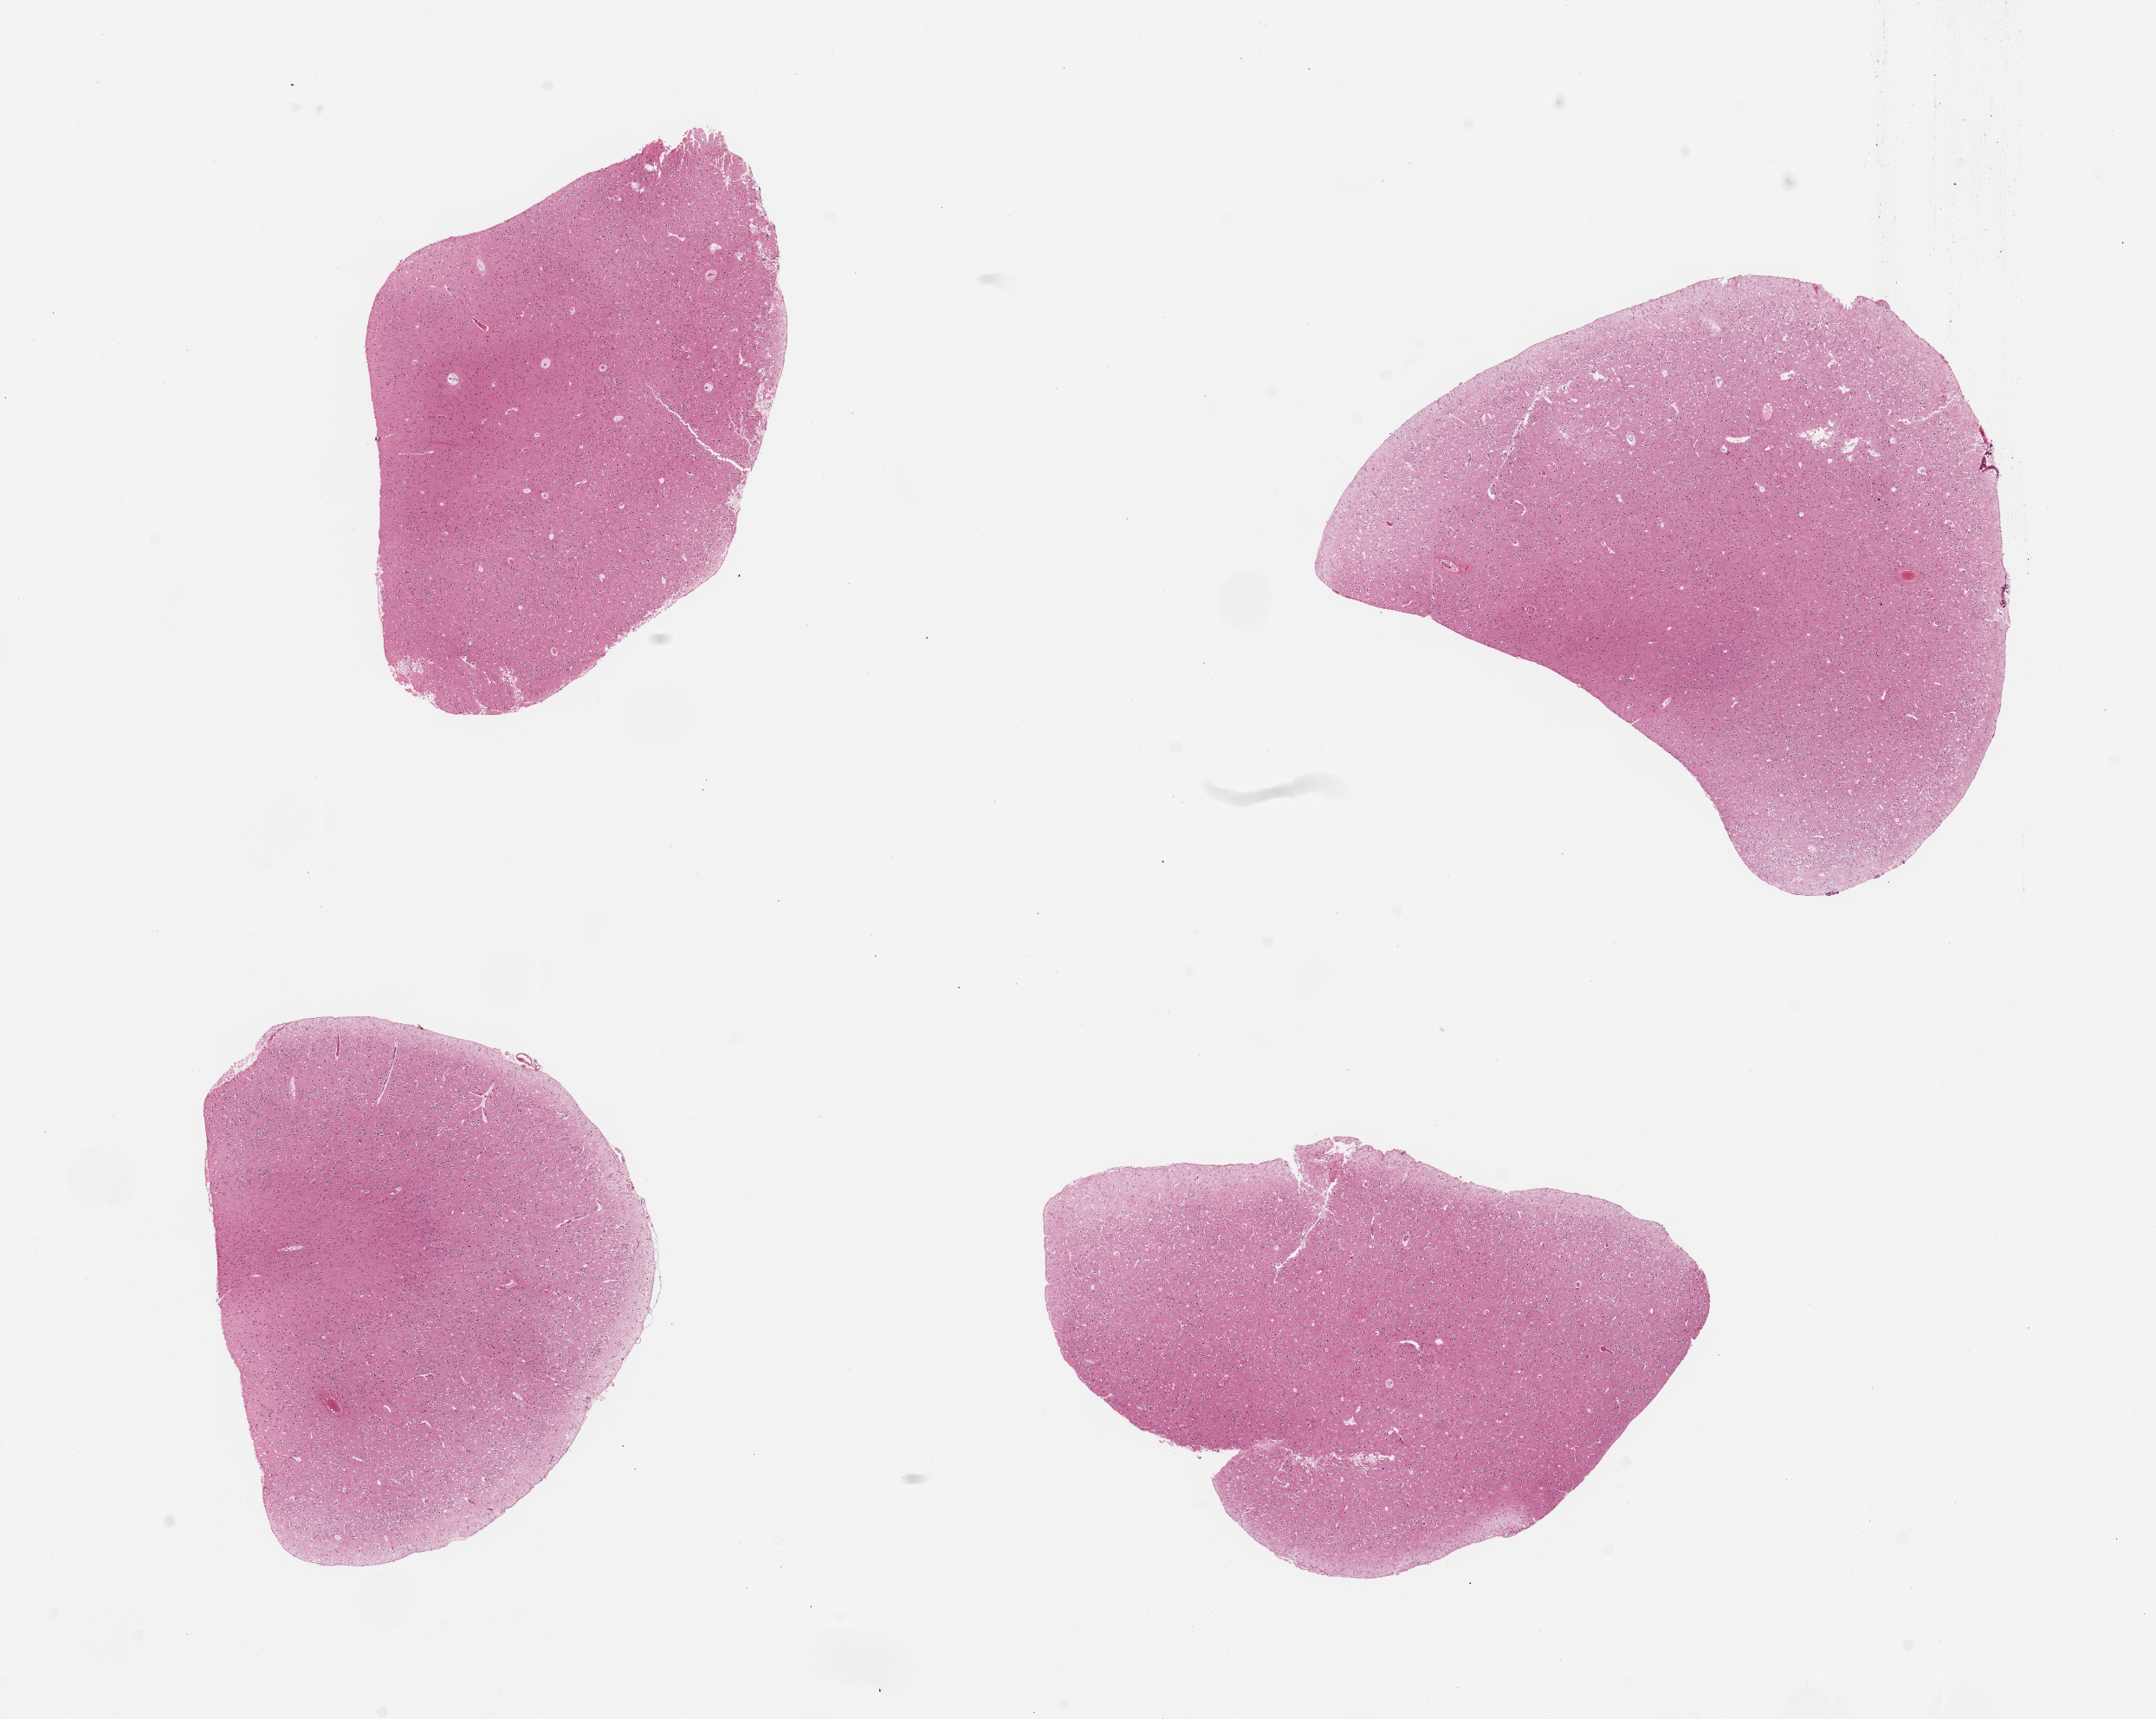
H&E whole-slide image — a low-resolution overview of the entire scanned area, about 19.7 x 15.7 mm. PAXgene-fixed, paraffin-embedded tissue. Target tissue: cerebral cortex. Tissue donor sample. Donor sex: female.
Reviewer comment on this tissue sample: 4 pieces, no abnormalities.